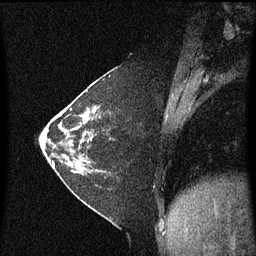
Breast MRI (dynamic contrast-enhanced), one sagittal slice; slice 23 of 60 in the series (ordered by position); dynamic contrast-enhanced series, image 2 of 3 at this slice position (ordered by acquisition); 1.5 T; TE 4.2 ms, TR 8.4 ms; 2 mm slice thickness; 256 × 256 image matrix, field of view 200 × 200 mm. Patient: female, 36 years. From the clinical record (not read from this slice): setting: breast cancer imaged before/during neoadjuvant chemotherapy; receptor status: HR-positive, HER2-negative.
Structures marked on this image (semi-automatically segmented with operator editing):
- analysis volume of interest (the breast-tissue region the enhancement analysis was run in; not a lesion): bounding box (x1, y1, x2, y2) in pixels: (66, 102, 112, 175)
- tumour enhancement mask (voxels above the 70 % enhancement threshold inside the analysis volume of interest): (83, 110, 96, 123)